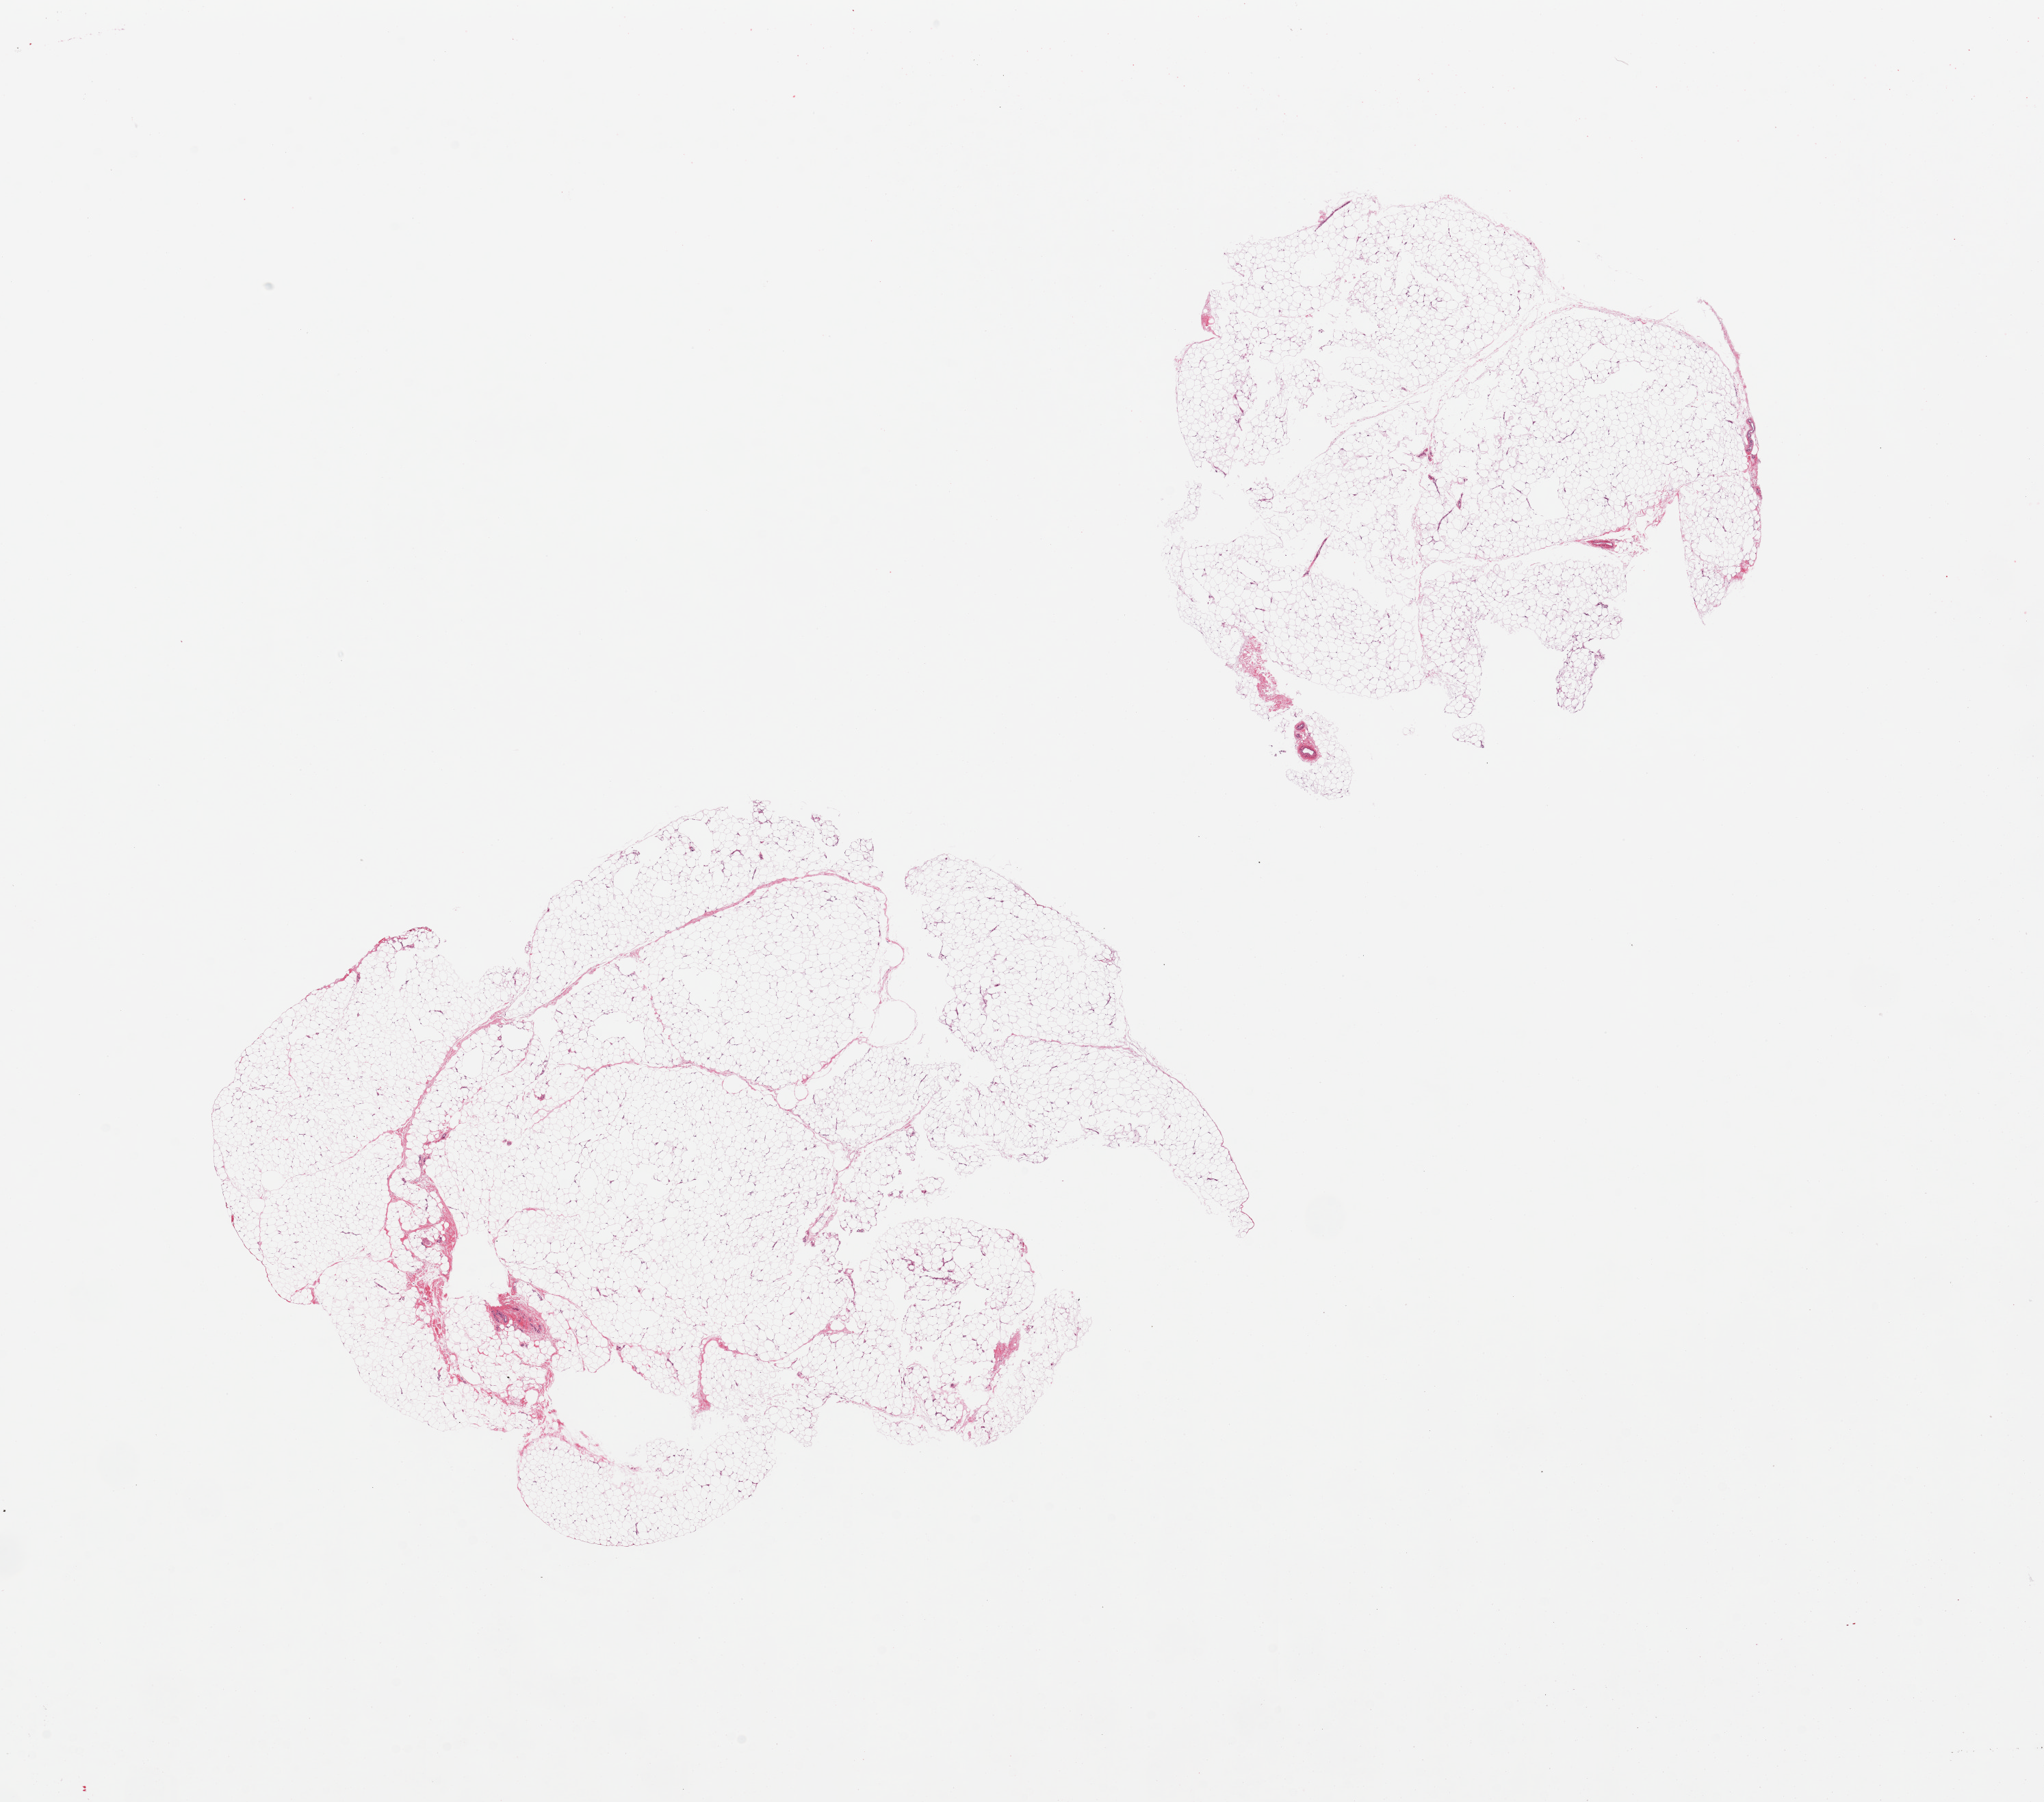
Haematoxylin and eosin whole-slide image — a low-resolution overview of the entire scanned area, about 23.6 x 20.8 mm (from a 20x scan); PAXgene-fixed, paraffin-embedded tissue; sampled site (target tissue): adipose tissue; donor tissue sample.
Reviewer comment on this tissue sample: 2 pieces.